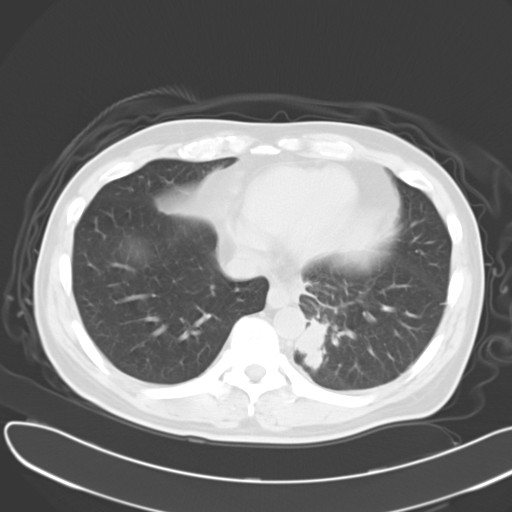
Chest CT, one axial slice. Position 10 of 30 along the scan axis. Reconstruction kernel B40f. 120 kVp. Lung window (W 1500 / L -600 HU). 512 × 512 image matrix, field of view 376 × 376 mm. Male patient, age 55 years. Case-level facts recorded for this patient, not image findings: clinical TNM (as recorded): T2 N3 M0; histopathological grade: G3.
Structures marked on this image (bounding box drawn by a radiologist):
- lung tumour (recorded histology: small cell carcinoma): box from (x=288, y=310) to (x=331, y=367) px